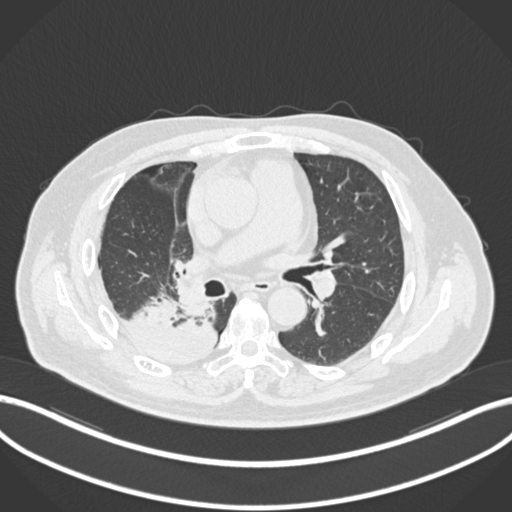
Chest CT, one axial slice; slice 102 of 218 in the series (ordered by position); reconstruction kernel B30f; lung window (W 1500 / L -600 HU); 512 × 512 image matrix, field of view 400 × 400 mm. Male patient, age 68 years. Case-level facts recorded for this patient, not image findings: clinical TNM (as recorded): T2a N0 M0.
Structures marked on this image (bounding box drawn by a radiologist):
- lung tumour (recorded histology: adenocarcinoma): box from (x=124, y=289) to (x=224, y=372) px